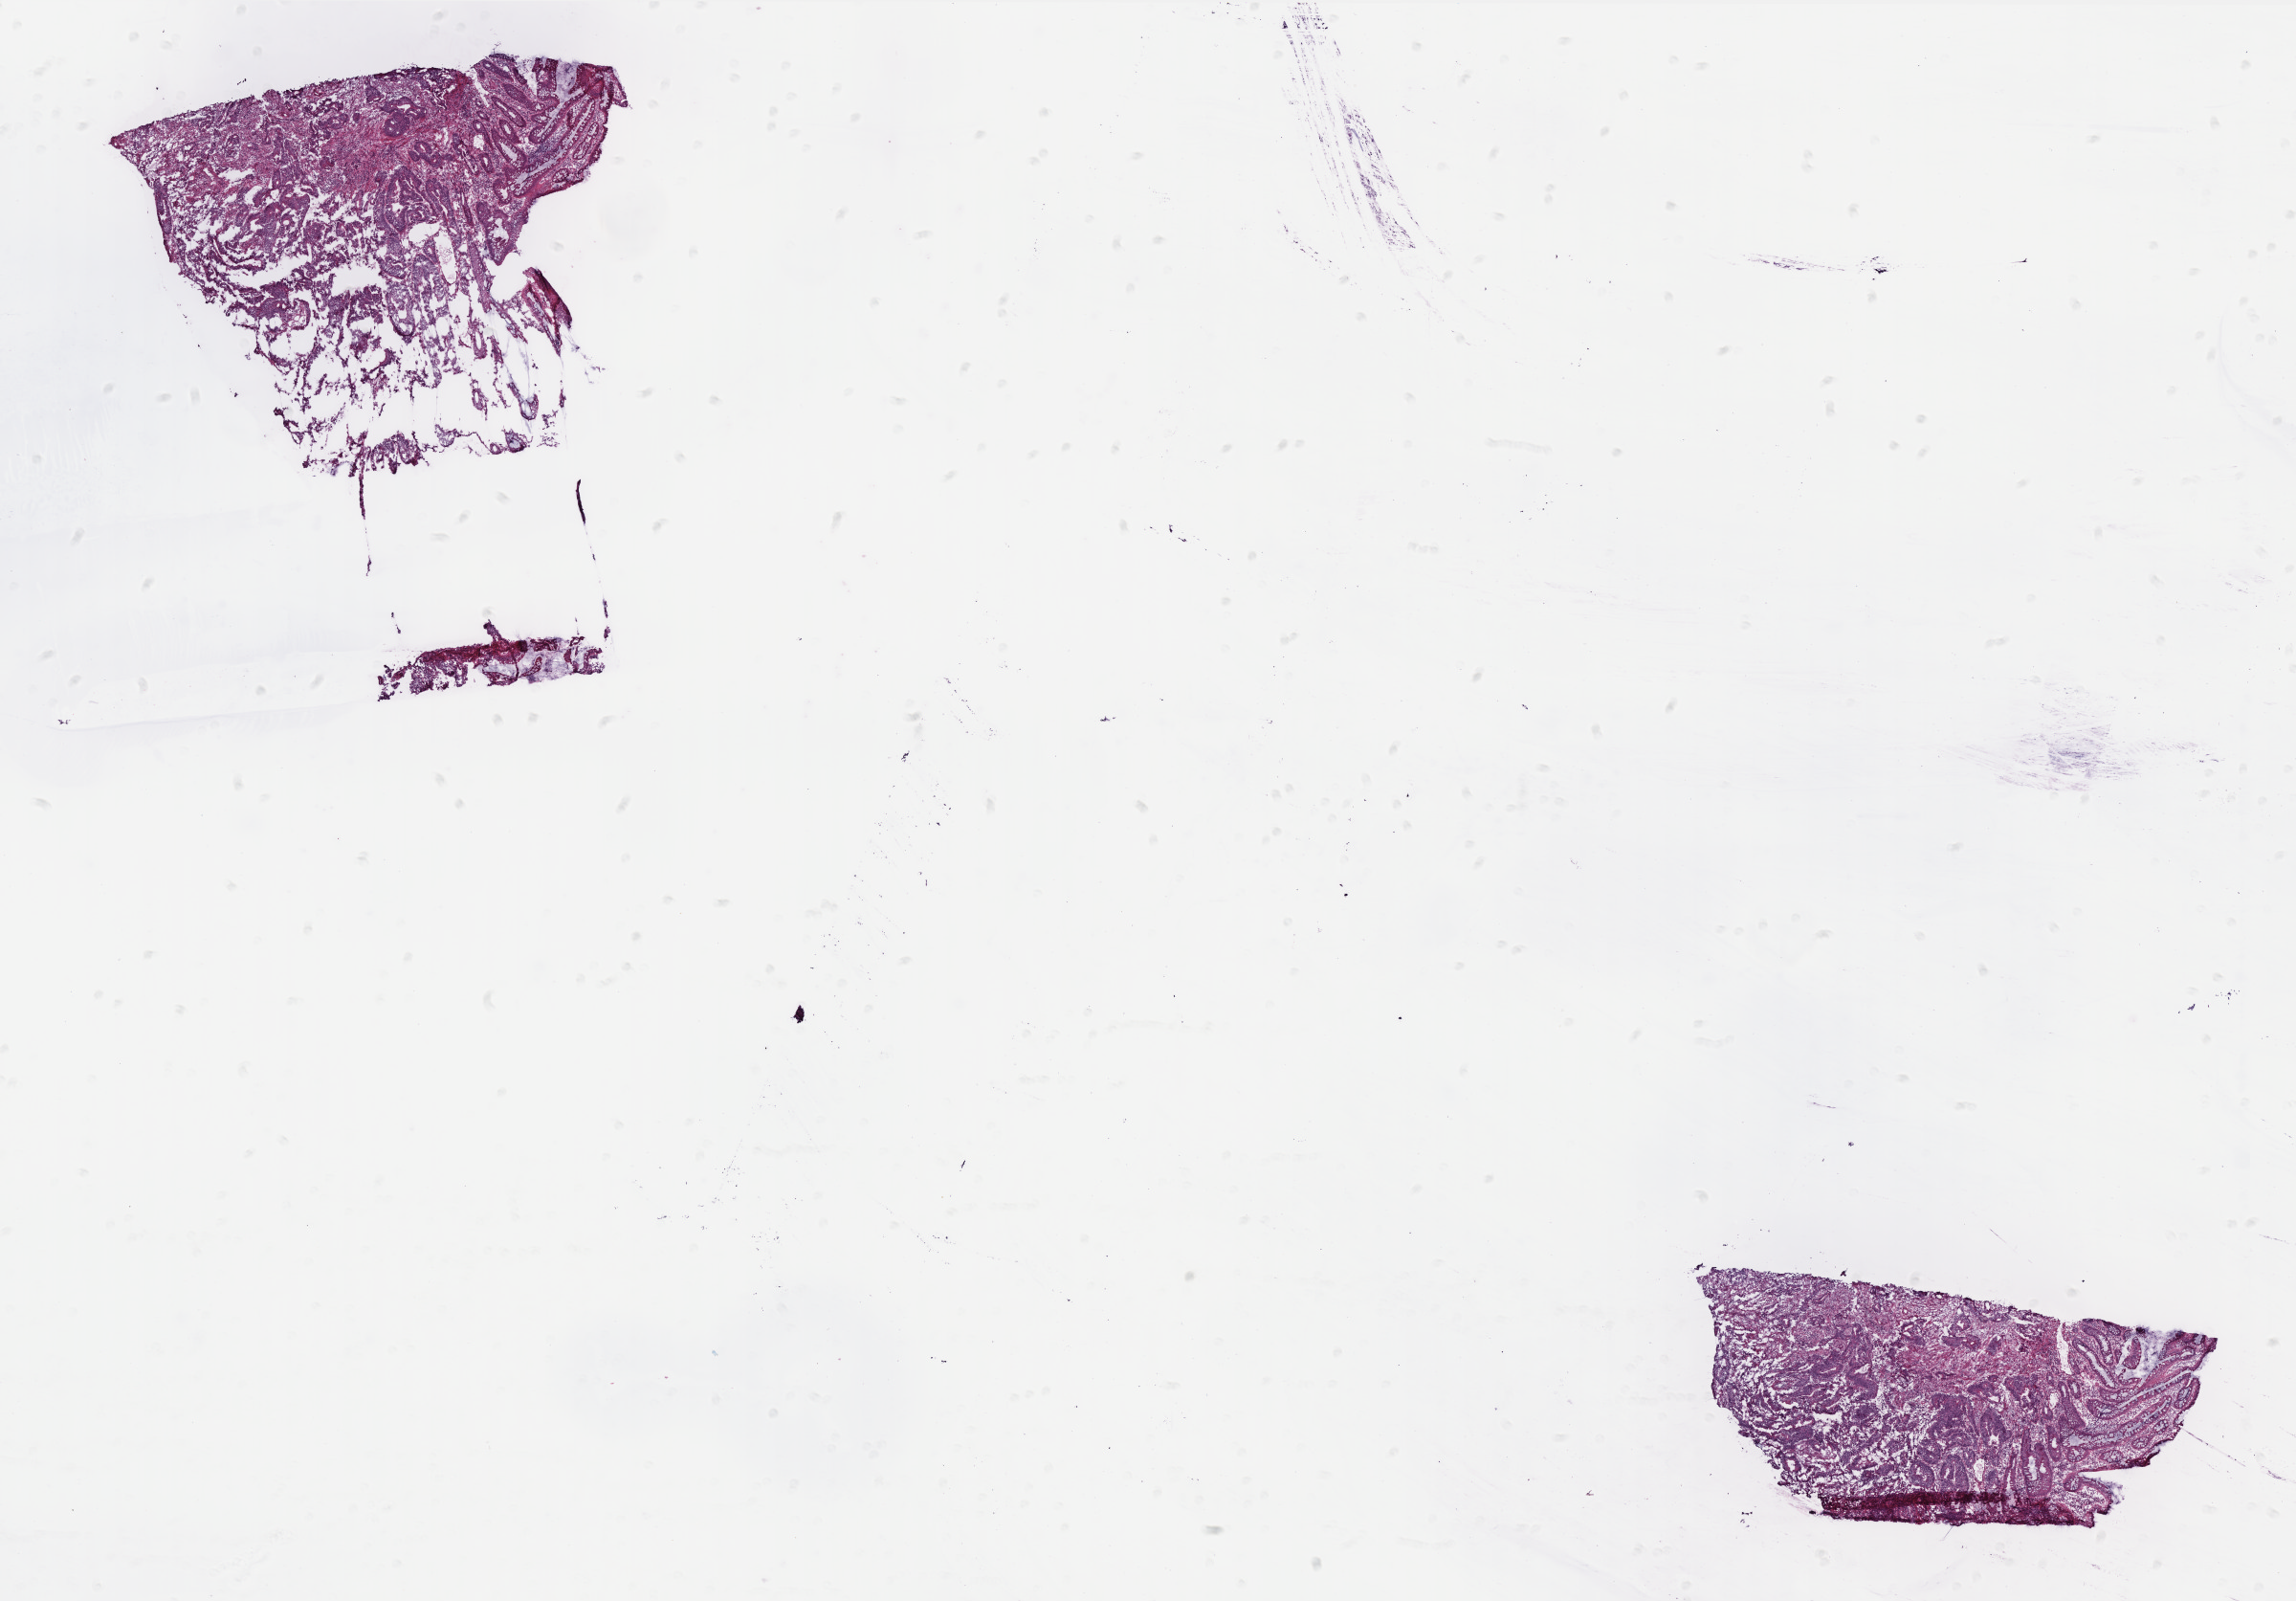
Hematoxylin and eosin (H&E) stained whole-slide image, a low-resolution overview of the entire scanned area, about 19.2 x 13.4 mm (from a 40x scan). Frozen section from the bottom of the tissue portion. Colon, primary tumour sample. Patient: male, age at initial diagnosis 66 years. Composition of this section per pathologist review: tumour cells 58%, tumour nuclei 75%, normal cells 25%, stromal cells 15%, necrosis 2%. Inflammatory infiltration, as recorded: lymphocyte infiltration 12%, monocyte infiltration 7%, neutrophil infiltration 1%.
* diagnosis: Adenocarcinoma, NOS (sigmoid colon)
* TNM: T3 N2 M0
* AJCC pathologic stage: IIIC
* lymph nodes positive (case pathology): 7 of 25 examined